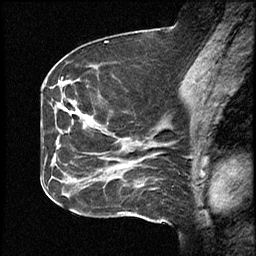
Breast MRI (dynamic contrast-enhanced), one sagittal slice; slice 23 of 46 in the series (ordered by position); dynamic contrast-enhanced study with each time point stored as its own series, time point 2 of 4 at this slice position (early post-contrast, ordered by acquisition time); 1.5 T; TE 4.2 ms, TR 18.3 ms; 256 × 256 image matrix, field of view 200 × 200 mm. Case-level facts recorded for this patient, not image findings: setting: breast cancer imaged before/during neoadjuvant chemotherapy; receptor status: HR-positive, HER2-negative.
Annotated regions visible in this slice (semi-automatically segmented with operator editing):
- analysis volume of interest (the breast-tissue region the enhancement analysis was run in; not a lesion): box from (x=64, y=80) to (x=111, y=200) px
- tumour enhancement mask (voxels above the 100 % enhancement threshold inside the analysis volume of interest): (x=77, y=111)–(x=82, y=116)